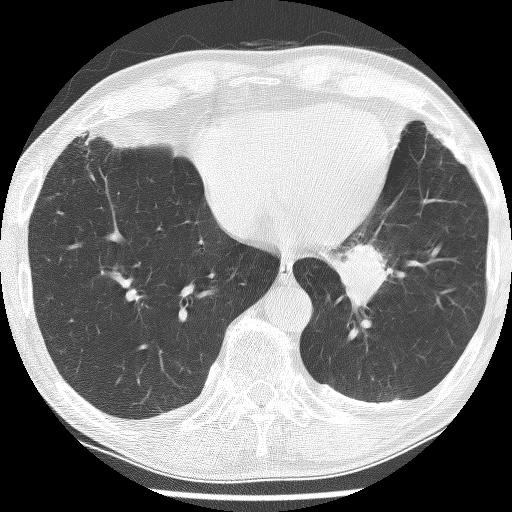
Chest CT (low-dose screening protocol), one axial image. First (baseline) screen. Lung window (W 1500 / L -600 HU). 2.5 mm slice thickness. Lung (sharp) reconstruction kernel (BONE). 512 × 512 image matrix. Male participant, aged 74 years at enrolment.
- Expert-annotated lung lesion, box from (x=315, y=223) to (x=419, y=316) px.
- Reader record for this screening exam (exam-level; its link to the box is not recorded): non-calcified nodule or mass ≥4 mm, left lower lobe, 30 × 27 mm, spiculated (stellate) margins, soft tissue attenuation.
- Lung cancer was diagnosed 151 days after this screen: adenocarcinoma, NOS, left lower lobe, stage IIIA (AJCC 6th edition), 49 mm at pathology.